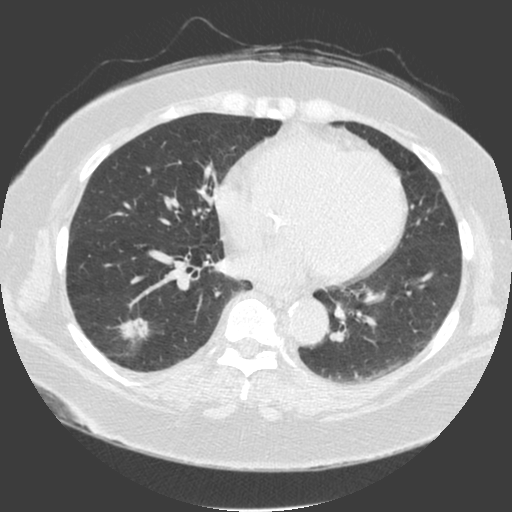
Low-dose screening chest CT, one axial slice. Slice 79 of 175 in the series (ordered by position). Lung window (W 1500 / L -600 HU). 2 mm slice thickness. 512 × 512 image matrix.
Annotated regions visible in this slice (outlined manually by an expert reader):
- lesion 1 (tumor, lower lobe of right lung): bounding box <120,318,148,338> (left, top, right, bottom; pixels)